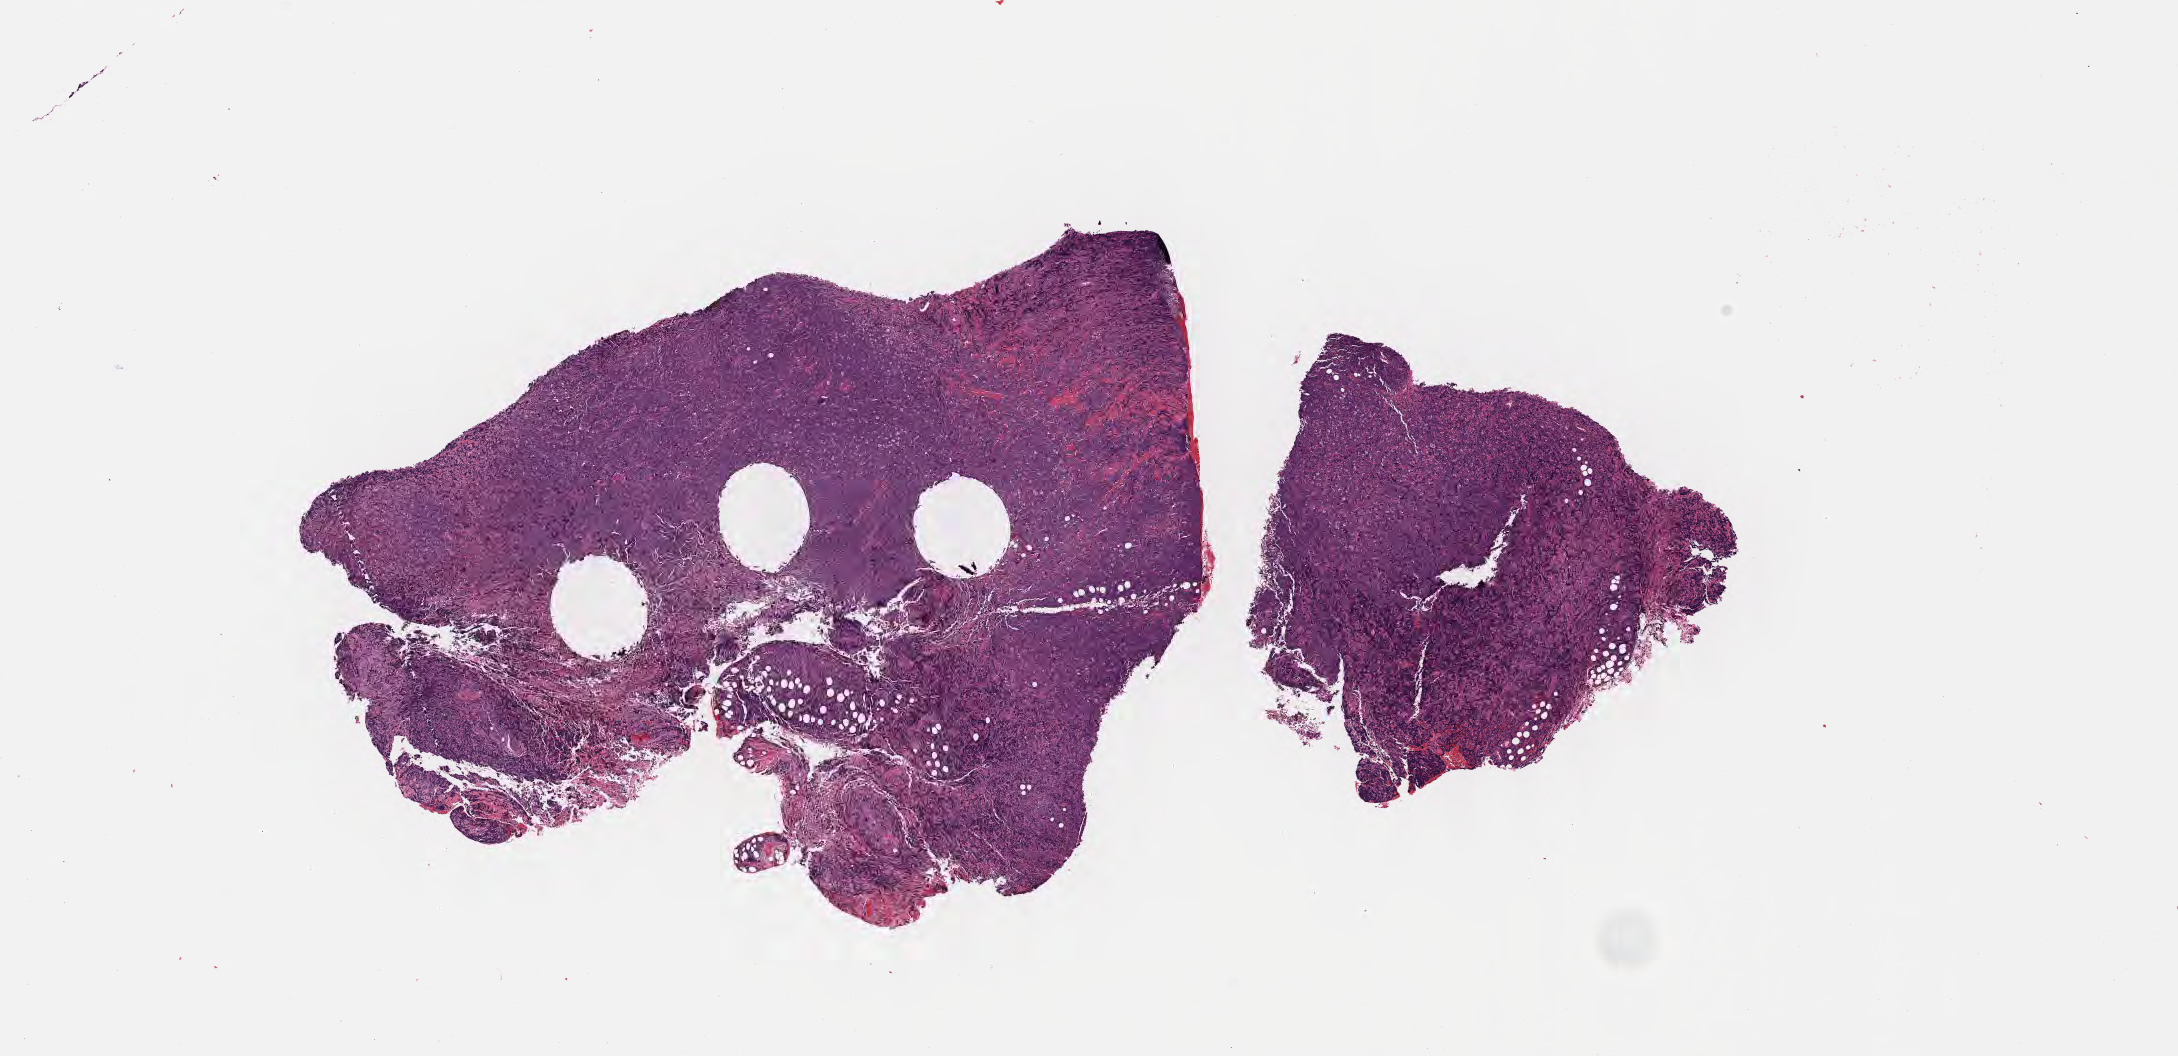
Hematoxylin and eosin (H&E) whole-slide image — shown as a low-resolution overview of the whole scanned area (about 17.6 x 8.5 mm). Formalin-fixed, paraffin-embedded (FFPE) tissue. Primary tumor. Anatomic site: cranium. Female, age 5 years at initial diagnosis. Slide review estimates, as recorded: tumor cells 95%, tumor nuclei 90%, stromal cells 2%, necrosis 3%, normal cells 0%. Infiltration values recorded for this section: lymphocyte infiltration 60%, monocyte infiltration 30%, neutrophil infiltration 5%.
Ann Arbor stage (patient): Stage IV. Diagnosis: Burkitt lymphoma, NOS.